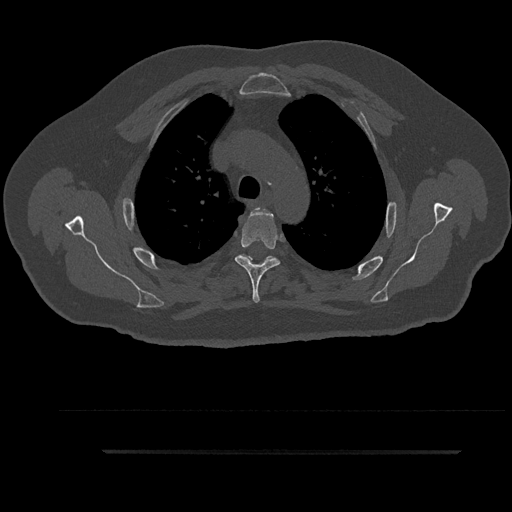
CT including the spine, one axial slice. Position 669 of 797 along the scan axis. Bone window (W 1800 / L 400 HU). 512 × 512 image matrix, field of view 432 × 432 mm. Patient: male, 63 years. Case-level facts recorded for this patient, not image findings: primary cancer: renal.
Outlined on this slice (semi-automatically segmented with operator editing):
- T3 vertebra: box from (x=249, y=208) to (x=258, y=258) px
- T4 vertebra: (x=235, y=208)–(x=281, y=303)
- T5 vertebra: (x=258, y=258)–(x=268, y=265)